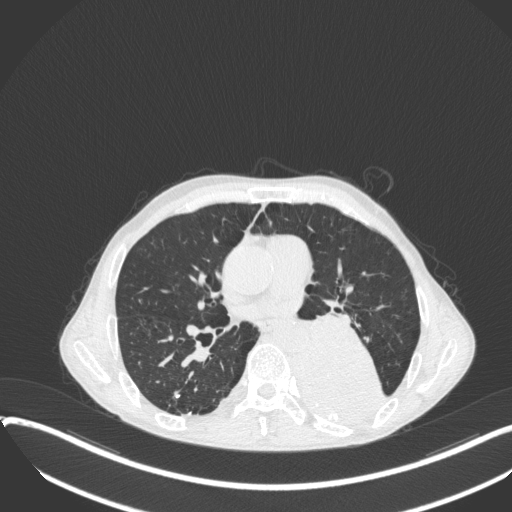
Chest CT, one axial slice; slice 192 of 400 in the series (ordered by position); reconstruction kernel B31f; 120 kVp; lung window (W 1500 / L -600 HU); 1 mm slice thickness; 512 × 512 image matrix, field of view 400 × 400 mm. Male patient, age 57 years. From the clinical record (not read from this slice): clinical TNM (as recorded): T4 N0 M0.
Outlined on this slice (bounding box drawn by a radiologist):
- lung tumour (recorded histology: squamous cell carcinoma): bounding box <286,330,390,428> (left, top, right, bottom; pixels)